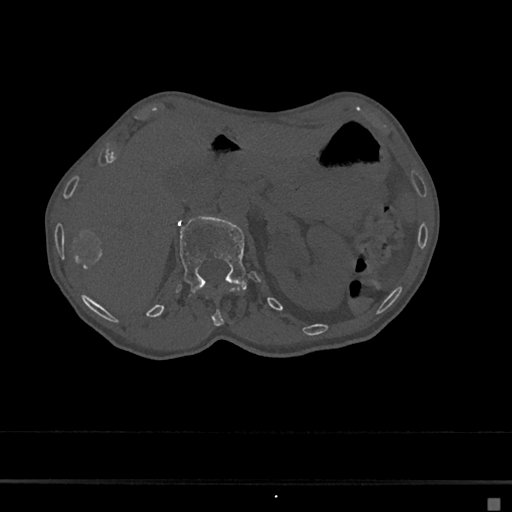
CT including the spine, one axial slice; slice 80 of 797 in the series (ordered by position); reconstruction kernel Br40s/3; 120 kVp; bone window (W 1800 / L 400 HU); 512 × 512 image matrix, field of view 360 × 360 mm. Female patient, age 68 years. From the clinical record (not read from this slice): primary cancer: renal.
Structures marked on this image (semi-automatic segmentation, software-assisted and operator-edited):
- L1 vertebra: bounding box (x1, y1, x2, y2) in pixels: (177, 216, 260, 293)
- T12 vertebra: (203, 287, 241, 327)